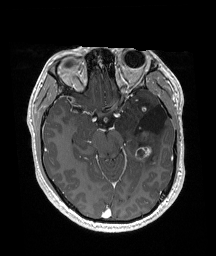
Brain MRI from a brain-tumour surgery series, one axial slice; slice 108 of 192 in the series (ordered by position); T1-weighted post-contrast; 1 mm slice thickness; 216 × 256 image matrix, field of view 211 × 250 mm. From the clinical record (not read from this slice): histopathology: Glioneuronal tumor; WHO grade: 2.
Annotated regions visible in this slice (outlined manually by an expert reader):
- previous resection cavity: bounding box (x1, y1, x2, y2) in pixels: (136, 105, 167, 133)
- tumour: (135, 106, 157, 162)